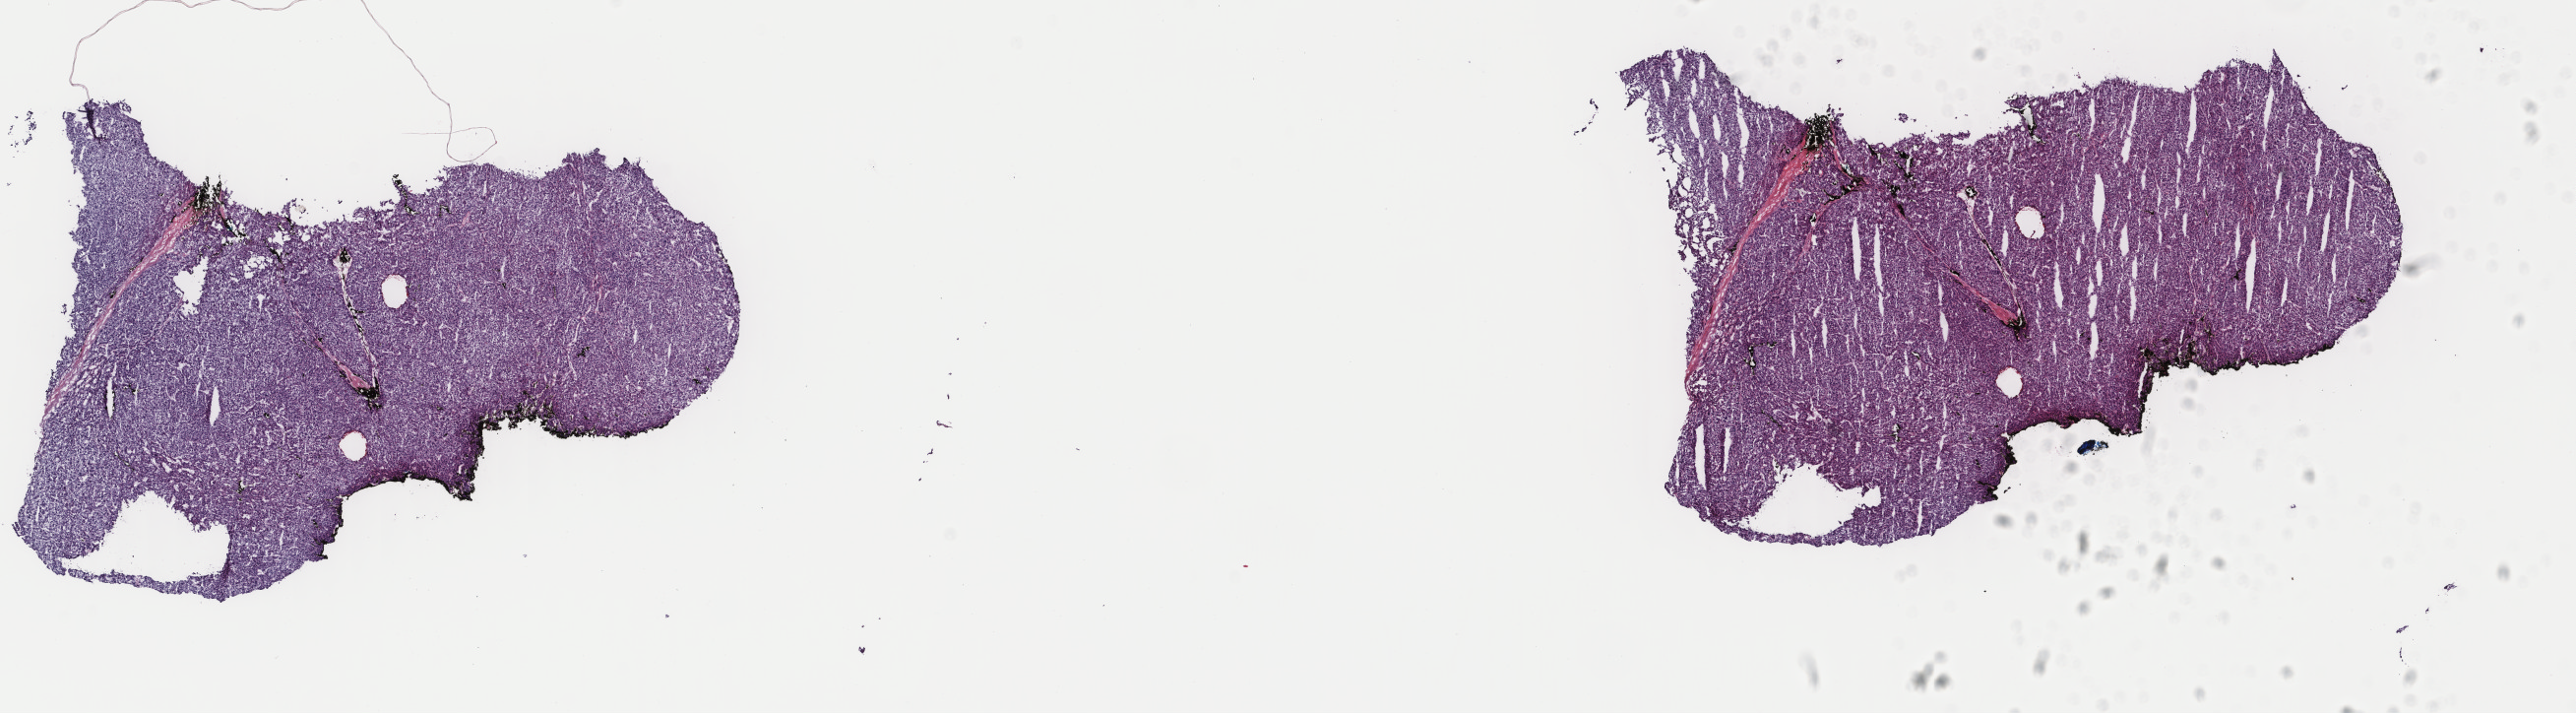
H&E whole-slide image — whole scanned area (about 20.8 x 5.7 mm, from a 40x scan) shown as a low-resolution overview. Frozen section from the top of the tissue portion. Primary tumour sample from the liver. Female, age 84 years at initial diagnosis. Histologic grade: G2 (moderately differentiated). Pathologist review of this section (percent, as recorded): tumour cells 85%, tumour nuclei 85%, normal cells 0%, stromal cells 15%, necrosis 0%. Inflammatory infiltration, as recorded: lymphocyte infiltration 1%, monocyte infiltration 0%, neutrophil infiltration 0%.
Pathologic diagnosis: Hepatocellular carcinoma, NOS. AJCC pathologic stage: I.